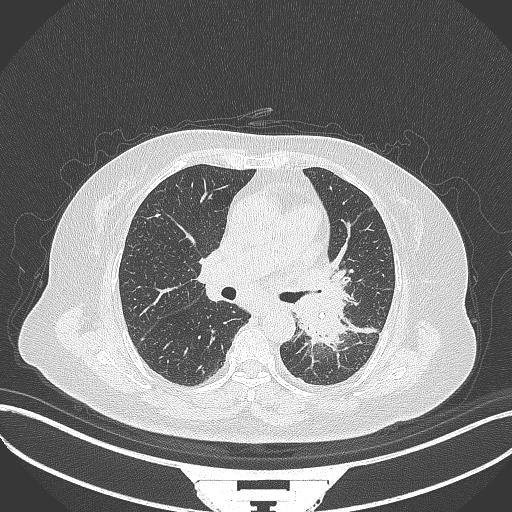
Chest CT, one axial slice. Position 199 of 322 along the scan axis. Reconstruction kernel B70f. 120 kVp. Lung window (W 1500 / L -600 HU). 1 mm slice thickness. 512 × 512 image matrix, field of view 400 × 400 mm. Patient: female, 69 years. Case-level facts recorded for this patient, not image findings: clinical TNM (as recorded): T2b N3 M1.
Structures marked on this image (rectangle marked by the reading radiologist):
- lung tumour (recorded histology: adenocarcinoma): bounding box <292,286,359,352> (left, top, right, bottom; pixels)